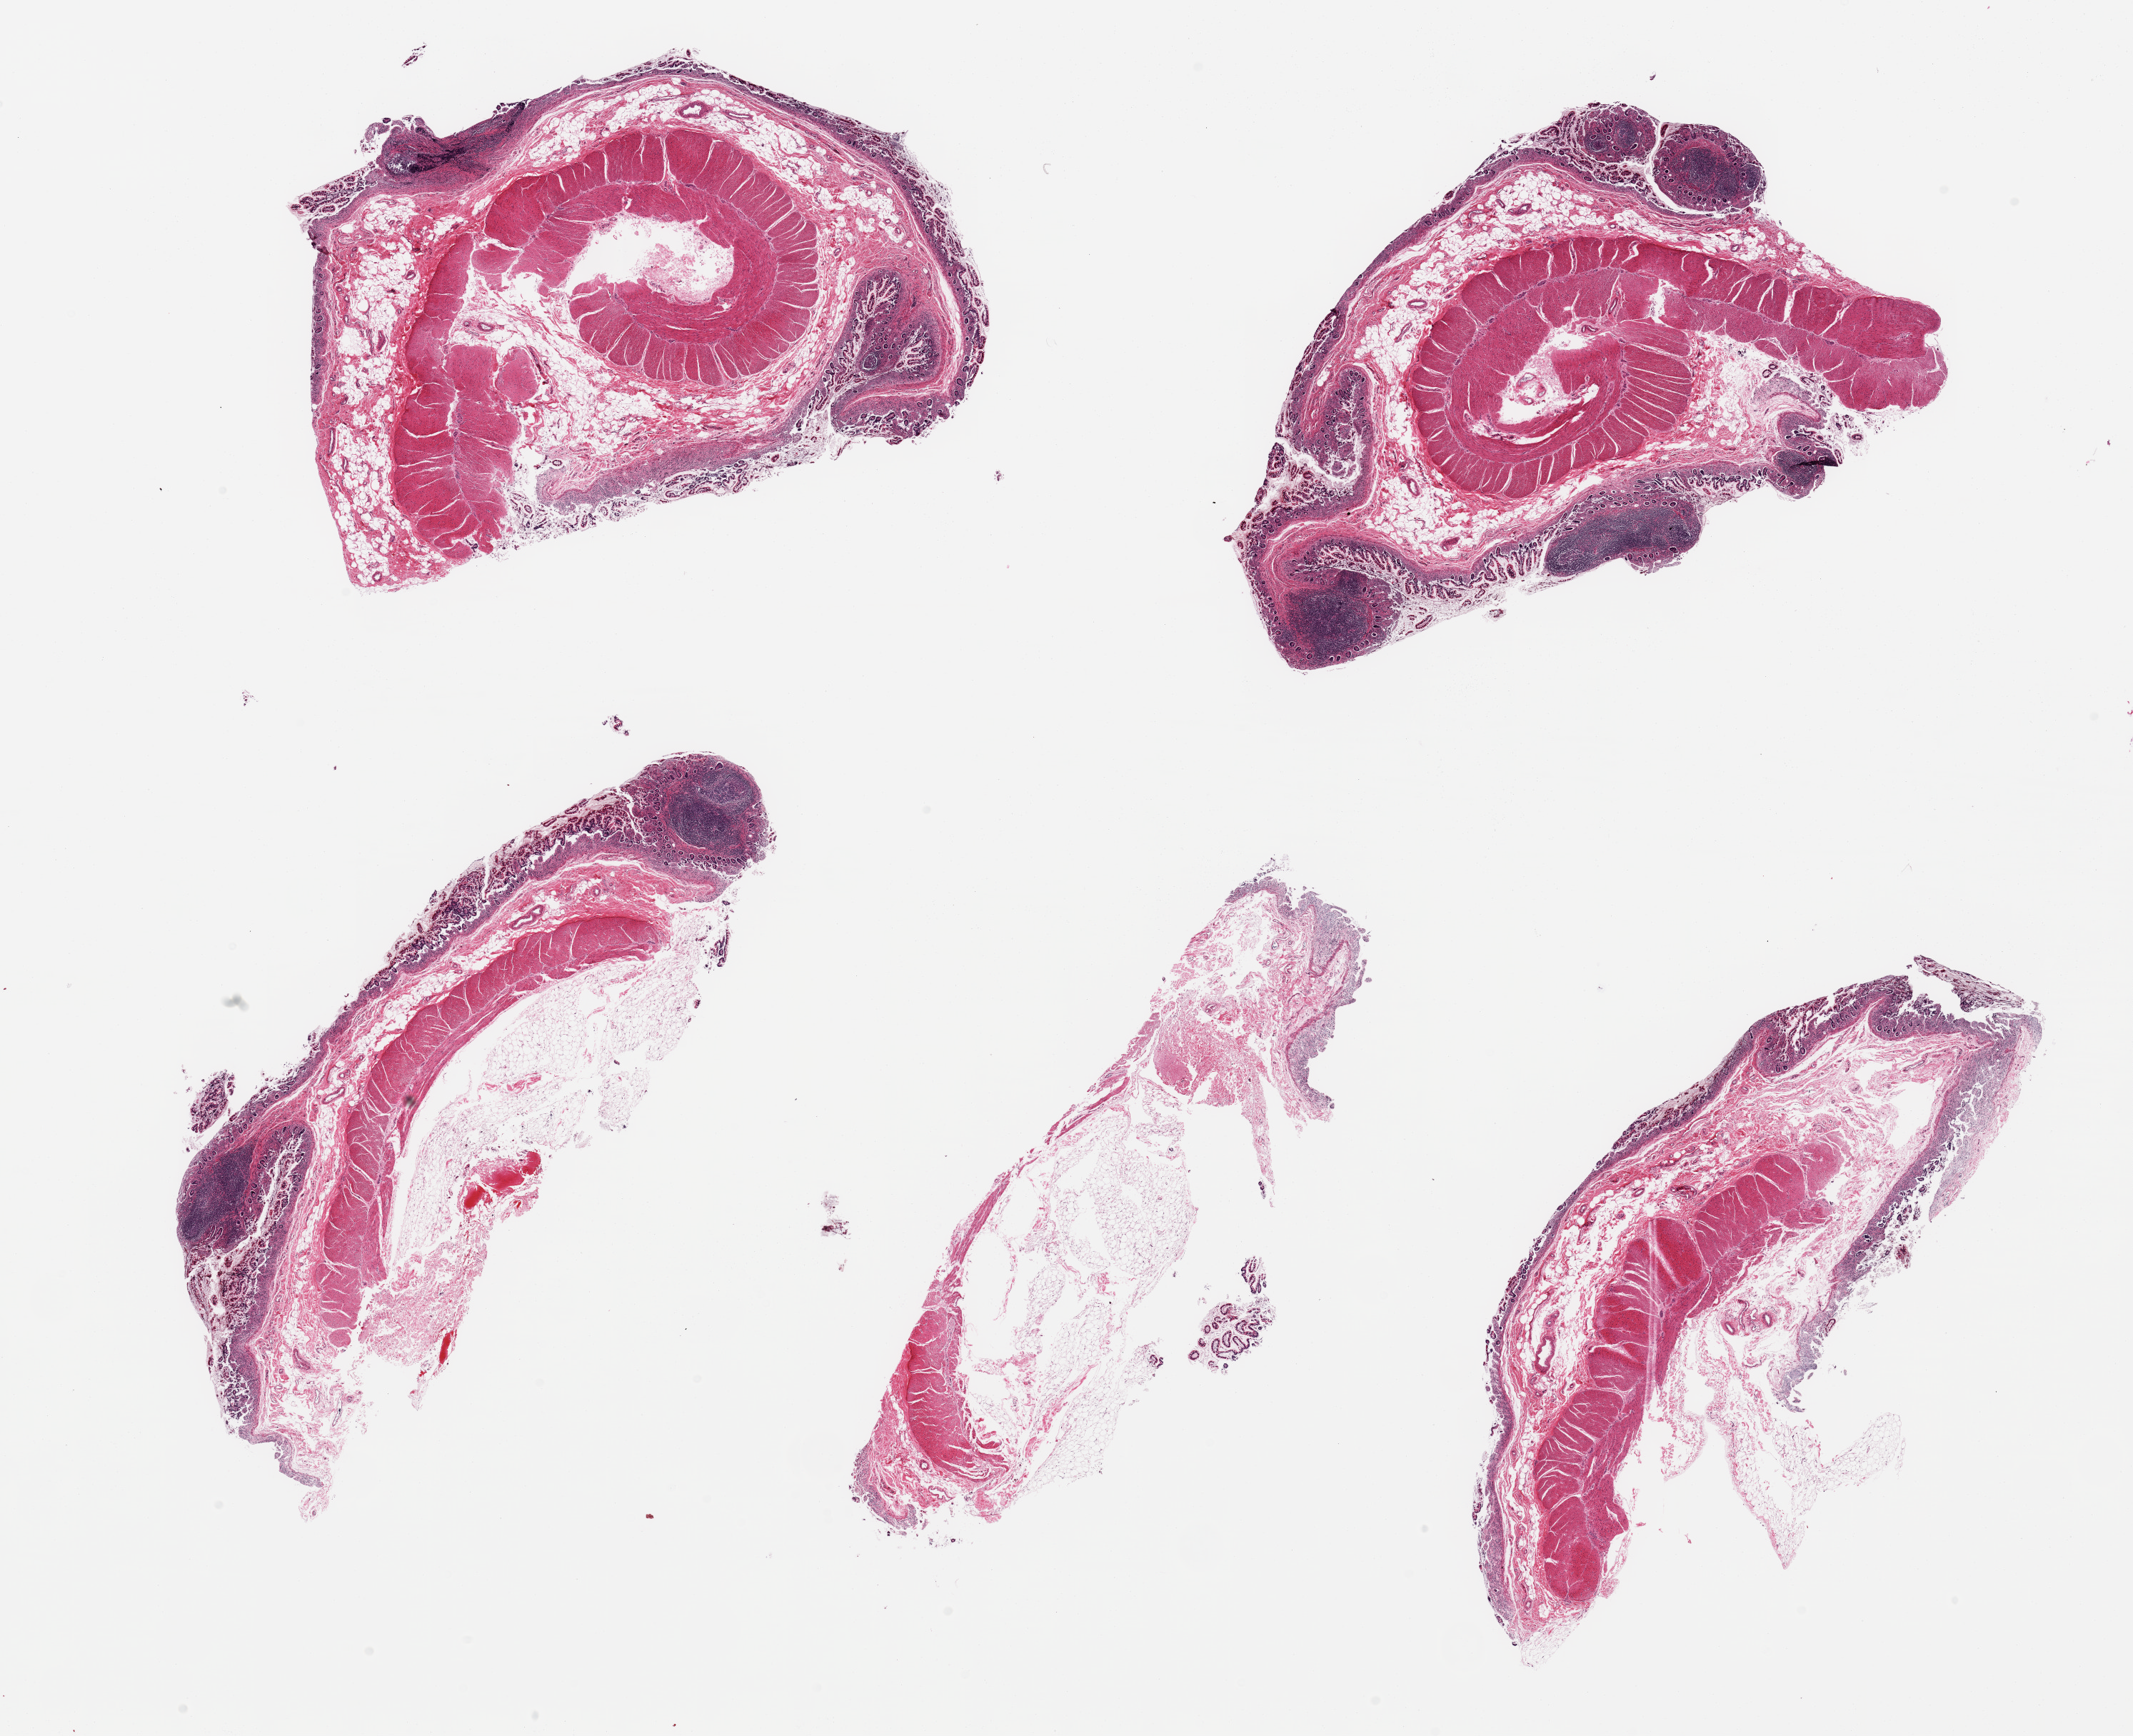
Whole-slide image, H&E stain, a low-resolution overview of the entire scanned area, about 23.6 x 19.2 mm; PAXgene-fixed paraffin-embedded (PFPE) section; sampled site (target tissue): ileum; tissue donor sample. Male donor.
Reviewer comment on this tissue sample: 5 pieces, target lymphoid aggregates well preserved, ~10-20% of tissue.